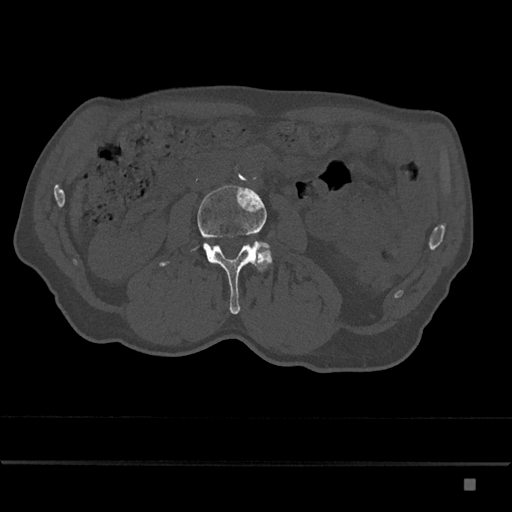
CT including the spine, one axial slice; slice 401 of 797 in the series (ordered by position); reconstruction kernel Br40s/3; 120 kVp; bone window (W 1800 / L 400 HU); 0.5 mm slice thickness; 512 × 512 image matrix, field of view 390 × 390 mm. Patient: male, 72 years. Case-level facts recorded for this patient, not image findings: primary cancer: prostate.
Annotated regions visible in this slice (semi-automatic segmentation, software-assisted and operator-edited):
- L3 vertebra: bounding box <159,185,270,314> (left, top, right, bottom; pixels)
- L4 vertebra: <256,247,272,272>